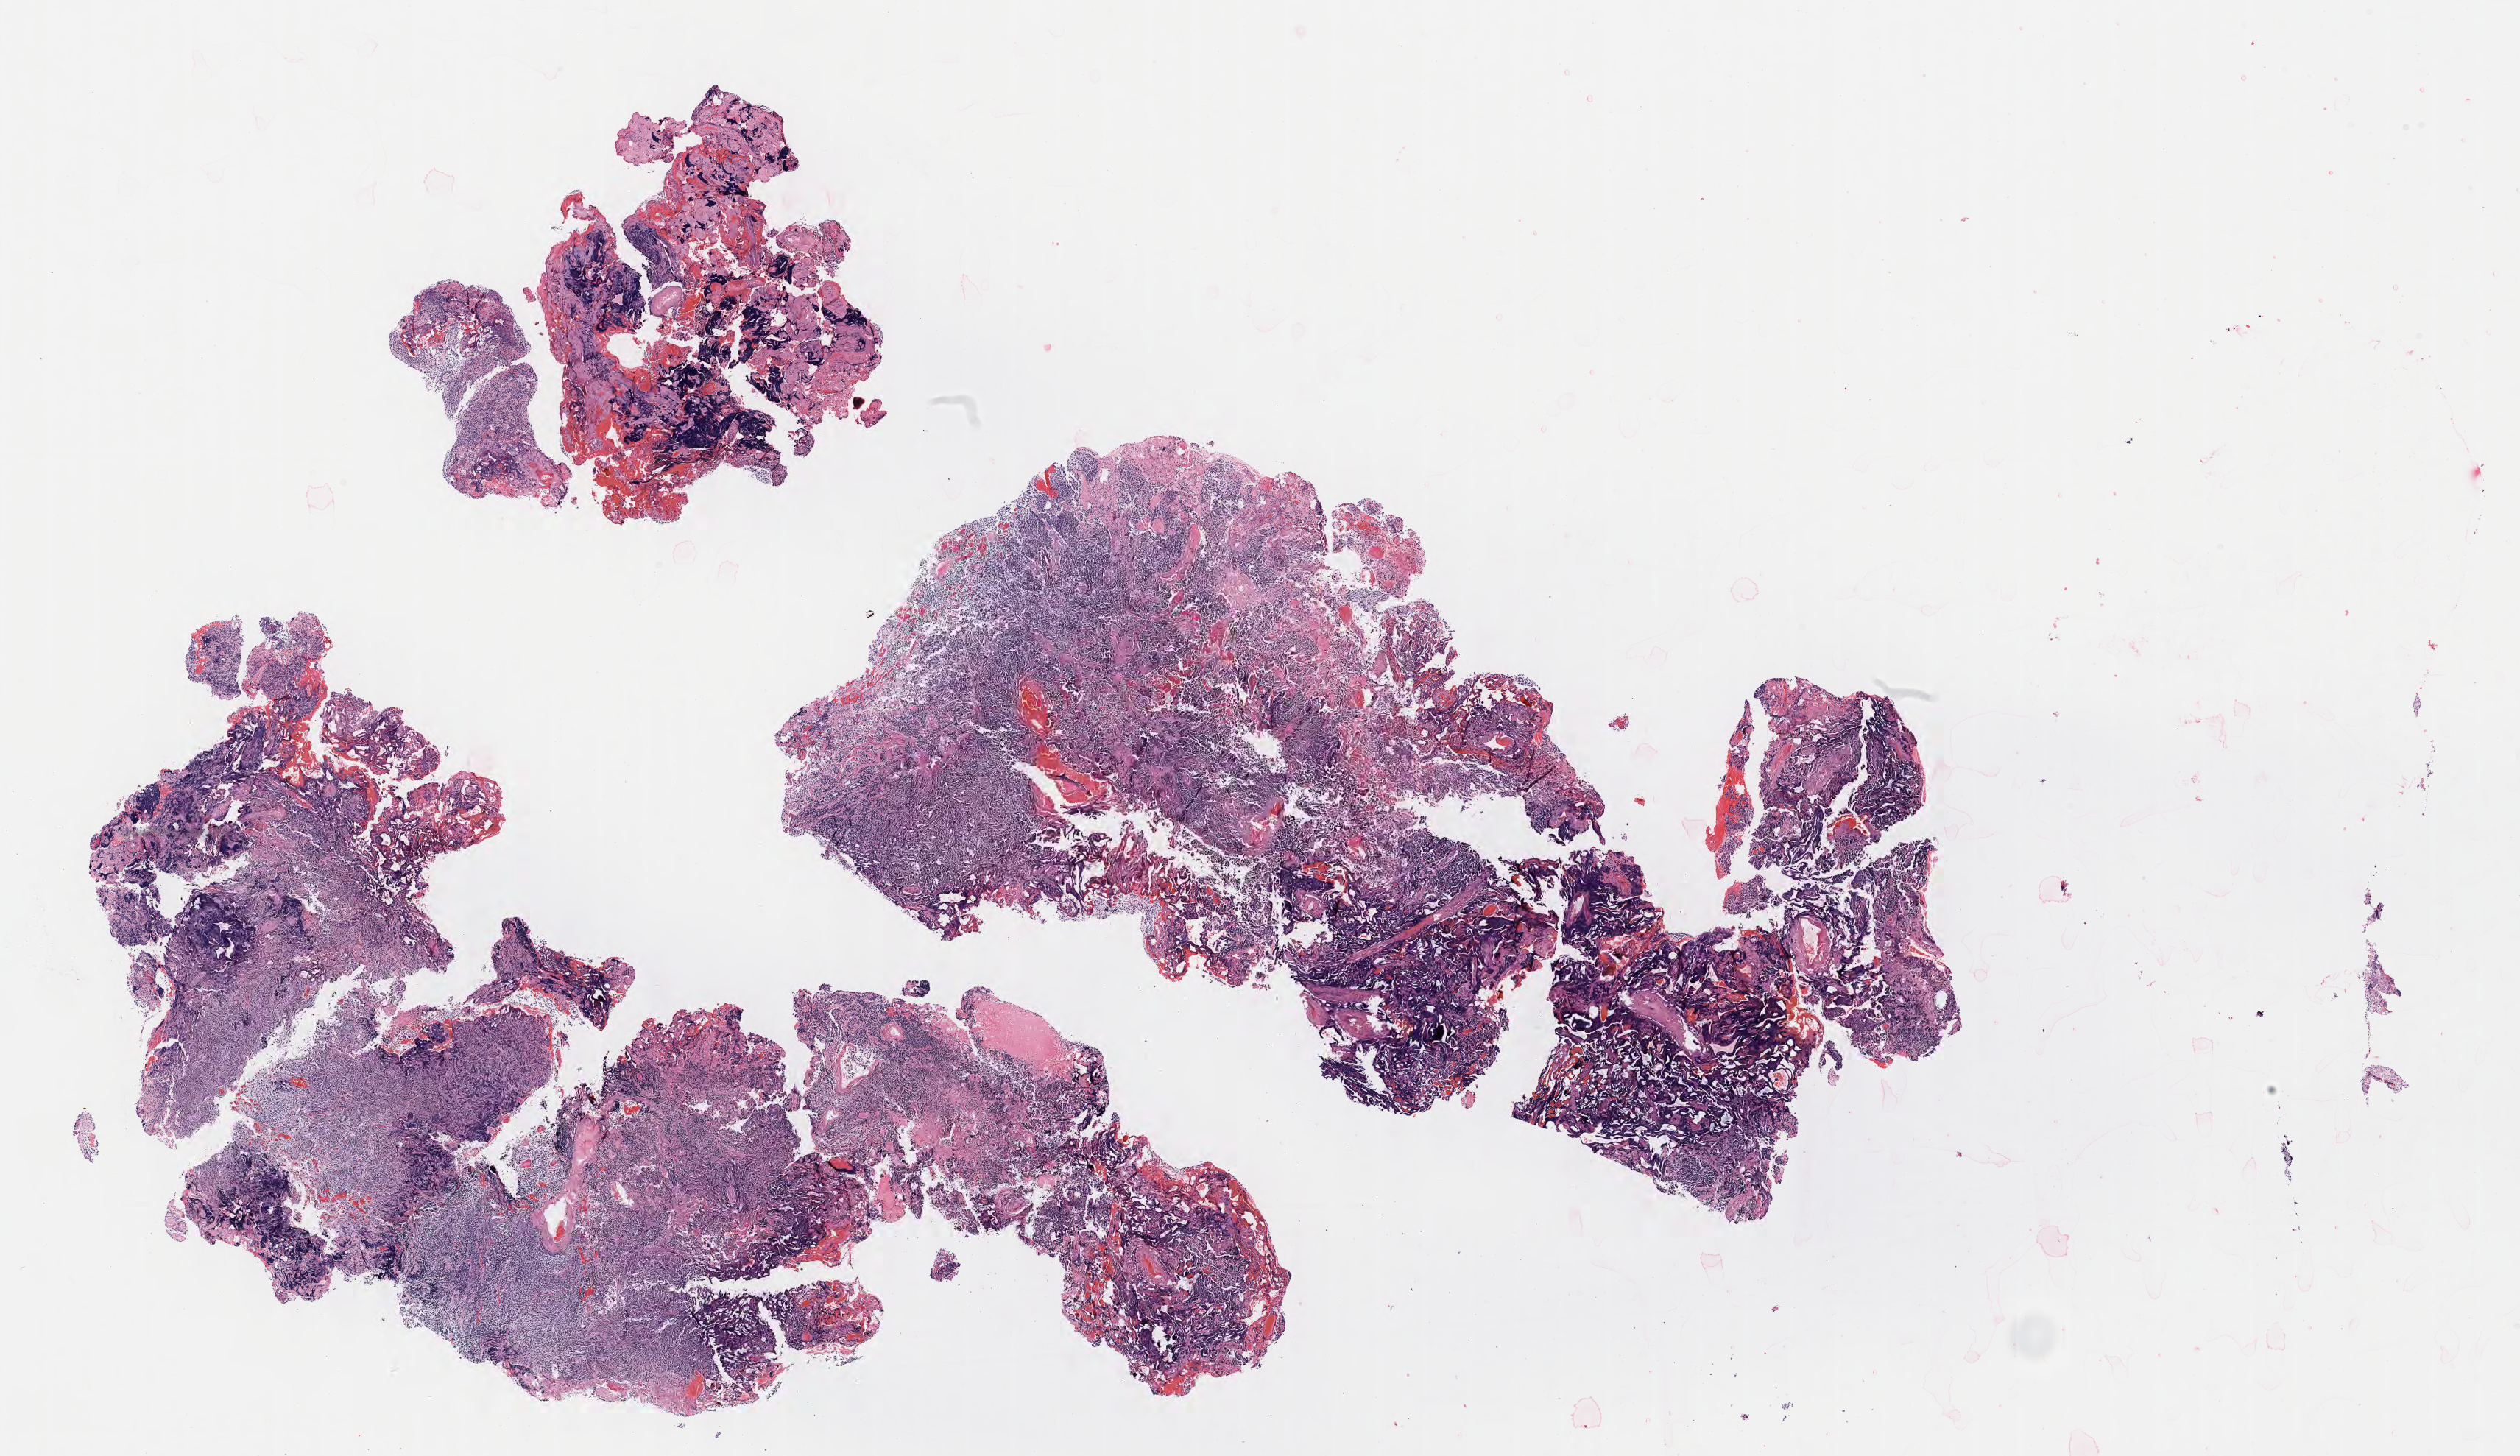
Digitized haematoxylin and eosin-stained section of tumor tissue from the brain — whole scanned area (about 27.7 x 16.0 mm) shown as a low-resolution overview. Formalin-fixed paraffin-embedded section. Male patient, age 141 months (11 years 9 months).
• recorded diagnosis: Medulloblastoma, NOS